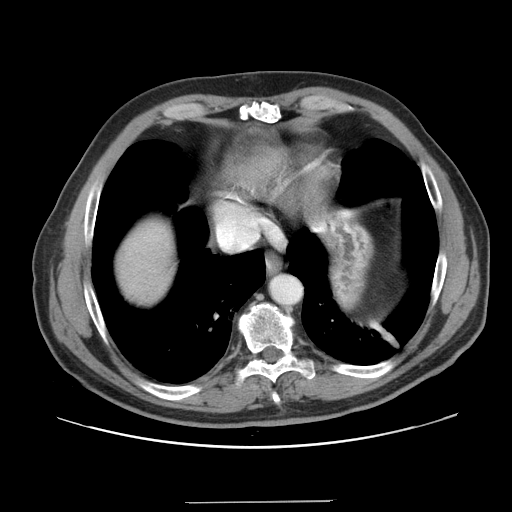
Contrast-enhanced abdominal CT, one axial slice; slice 143 of 151 in the series (ordered by position); soft-tissue window (W 400 / L 40 HU); 512 × 512 image matrix. Male patient, age 63 years. Case-level facts recorded for this patient, not image findings: diagnosis: colorectal cancer liver metastases, imaged before liver resection; multiple liver metastases: no; largest metastasis: 2.1 cm; disease in both lobes: no.
Annotated regions visible in this slice (outlined manually by an expert reader):
- hepatic veins: bounding box <218,217,258,250> (left, top, right, bottom; pixels)
- liver: <114,221,176,308>
- planned liver remnant (the part of the liver to remain after resection): <113,221,176,308>